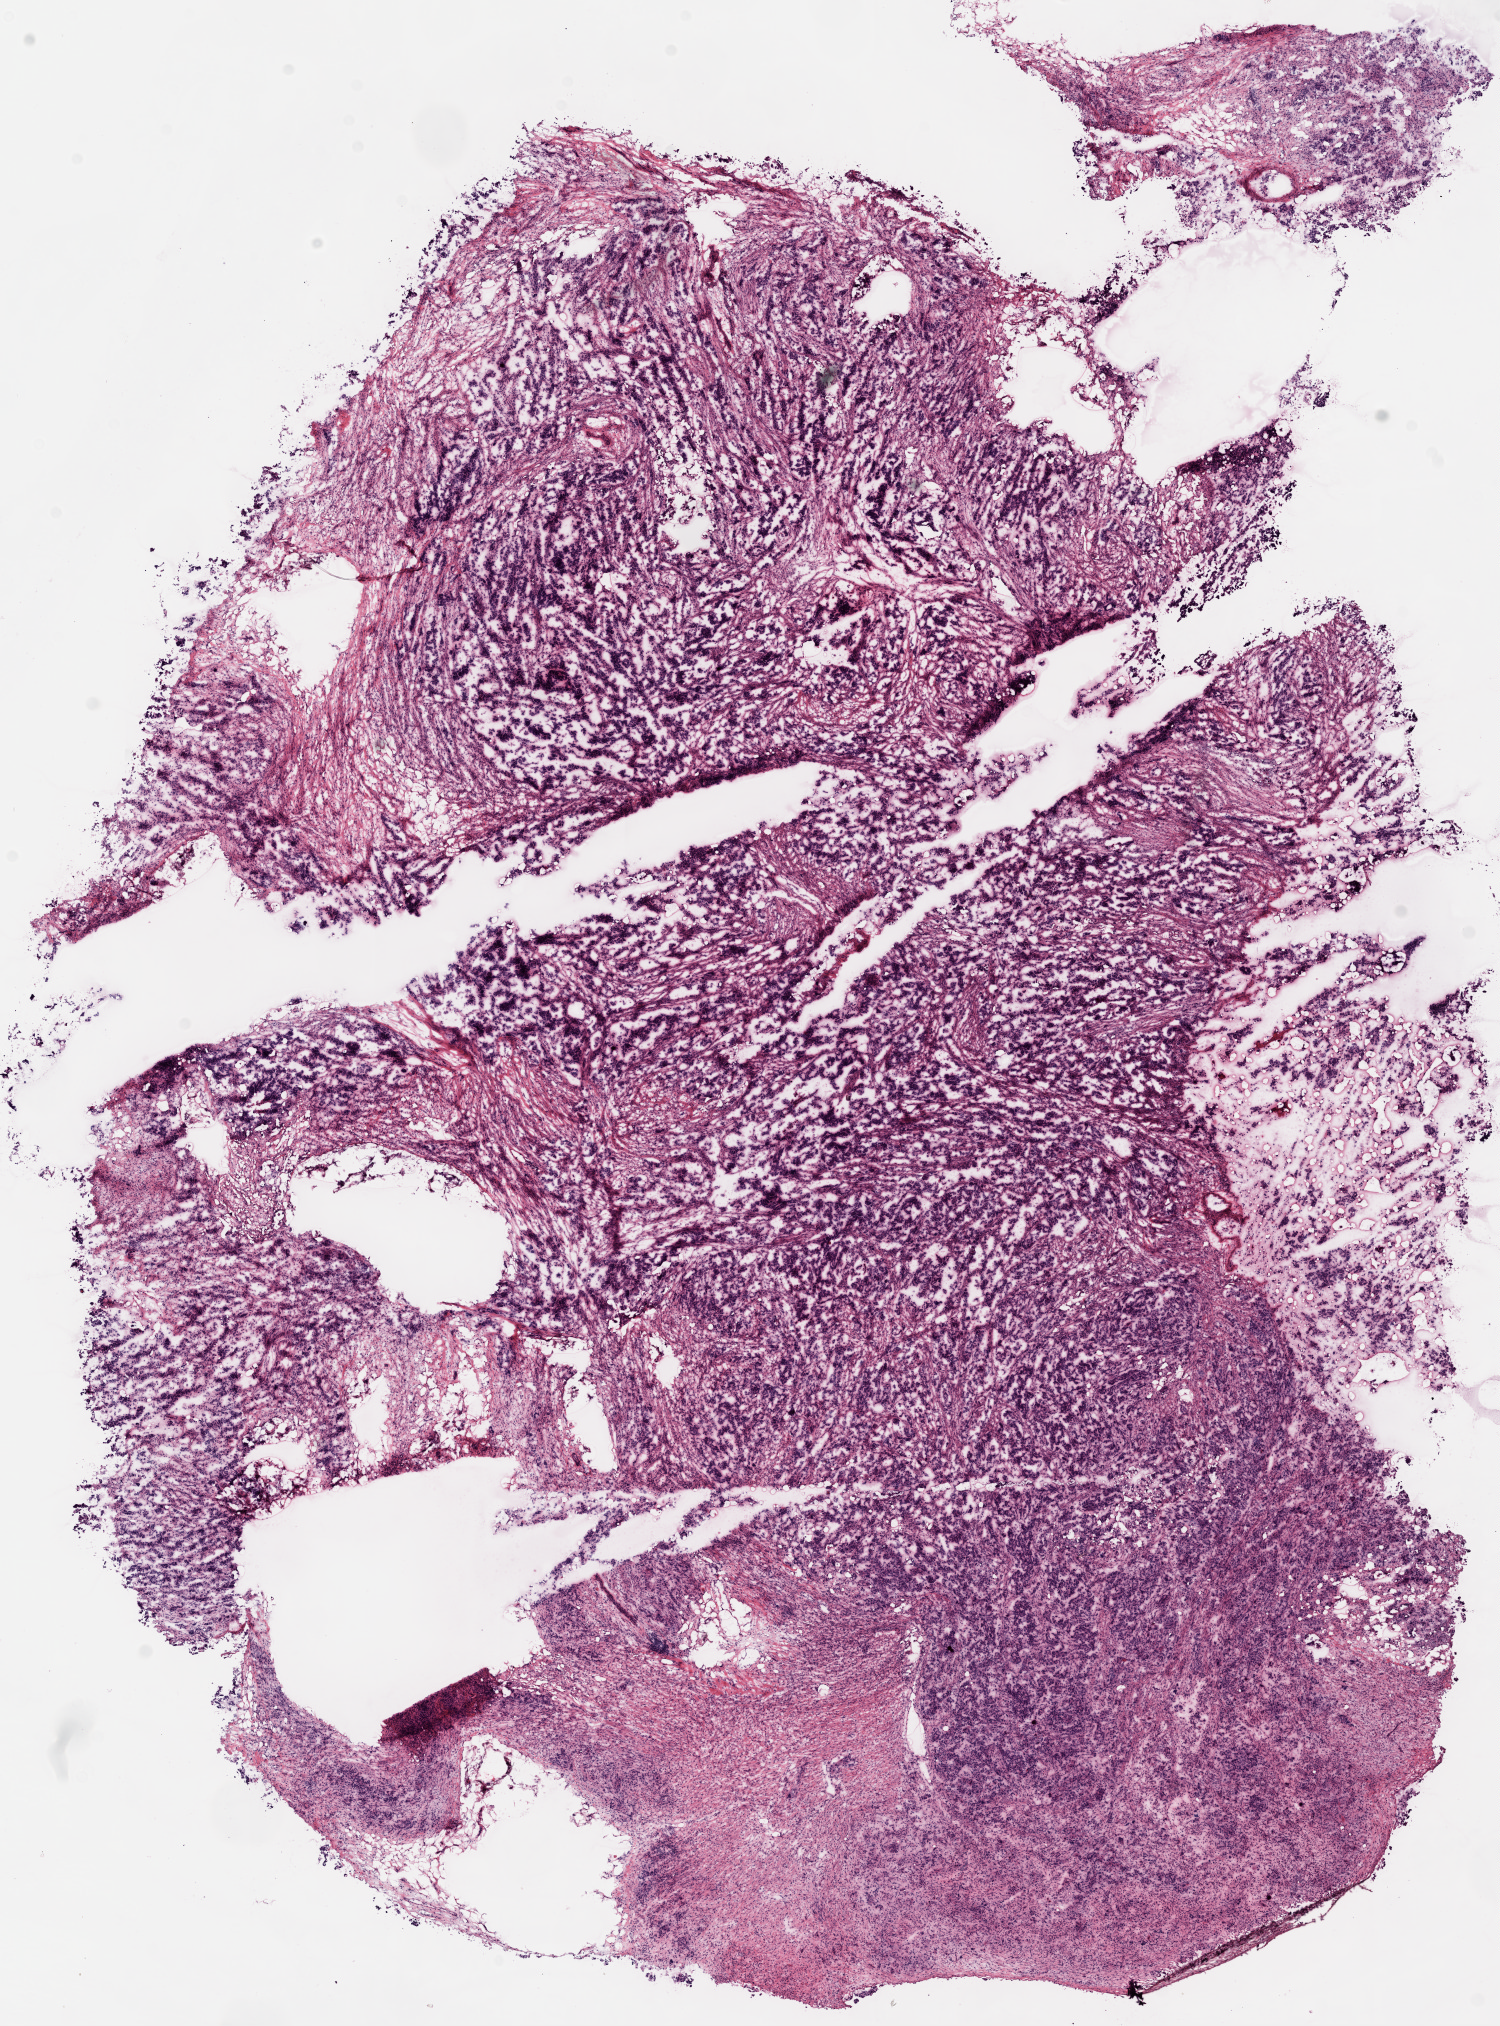
Digitized H&E-stained tissue section (whole slide), a low-resolution overview of the entire scanned area, about 12.0 x 16.3 mm (acquisition: 20x scan); frozen section; sample: primary tumour, ovary. Patient: female, age at initial diagnosis 53 years. Histologic grade: G3 (poorly differentiated). Pathologist review of this section (percent, as recorded): tumour cells 80%, tumour nuclei 80%, normal cells 0%, stromal cells 20%, necrosis 0%.
FIGO stage: IIIC. Pathologic diagnosis: Serous cystadenocarcinoma, NOS.